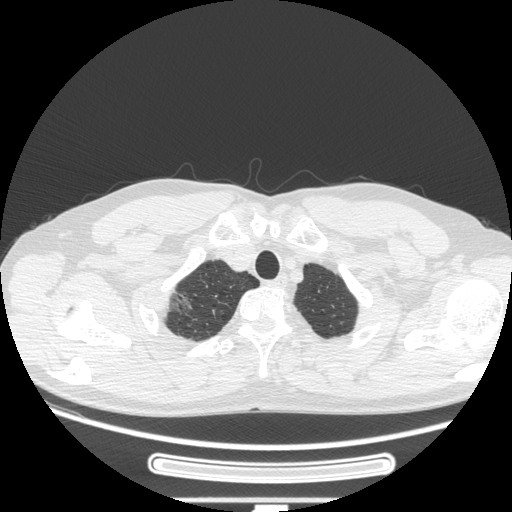
Chest CT, one axial slice. Position 239 of 269 along the scan axis. Lung window (W 1500 / L -600 HU). 1.25 mm slice thickness. 512 × 512 image matrix. Male patient, age 53 years. From the clinical record (not read from this slice): clinical TNM (as recorded): T1c N0 M0; histopathological grade: G2.
Annotated regions visible in this slice (bounding box drawn by a radiologist):
- lung tumour (recorded histology: adenocarcinoma): bounding box <167,289,195,322> (left, top, right, bottom; pixels)